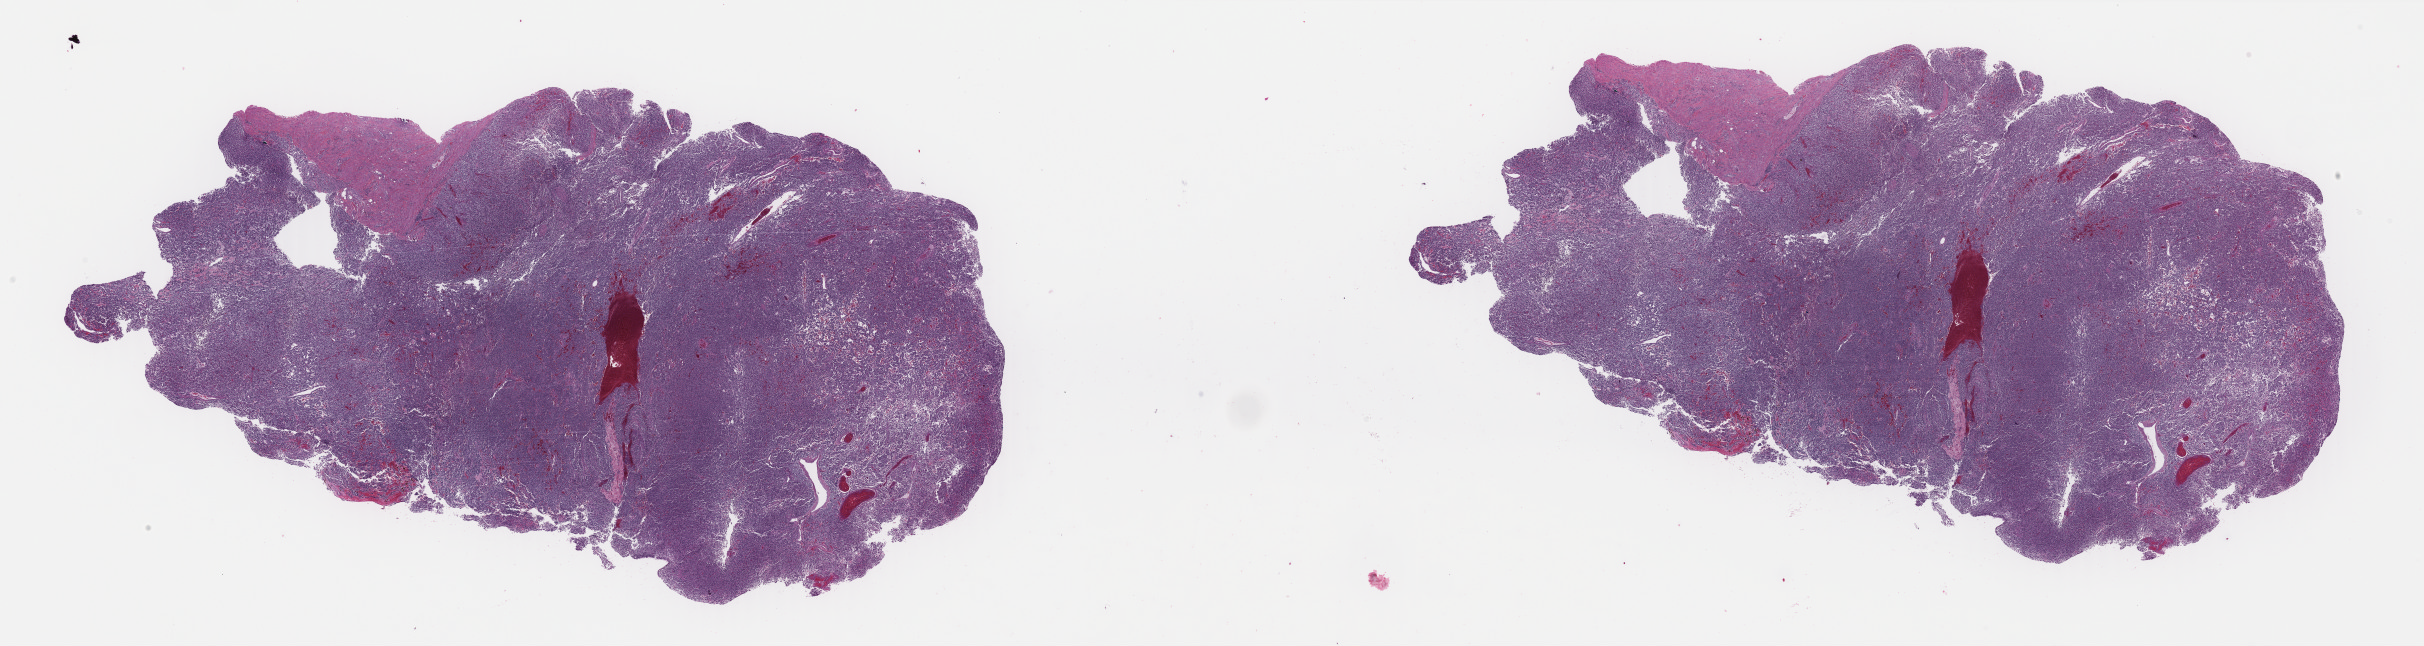
H&E whole-slide image — shown as a low-resolution overview of the whole scanned area (about 38.4 x 10.2 mm, from a 40x scan). Formalin-fixed paraffin-embedded (FFPE) diagnostic section. Retroperitoneum and peritoneum, primary tumour sample. Male patient; age at initial diagnosis 56 years.
Pathologic diagnosis: Extra-adrenal paraganglioma, NOS (retroperitoneum).